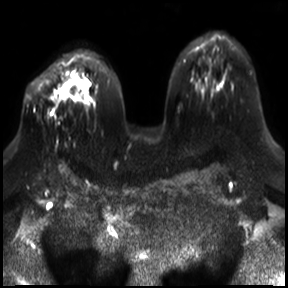
Breast MRI, one axial slice; position 20 of 30 along the scan axis; diffusion-weighted series; image 2 of 4 stored at this slice position (different b-values; order by instance number); 3 T; 4 mm slice thickness; 288 × 288 image matrix. Female patient.
Annotated regions visible in this slice (expert manual segmentation):
- tumour on diffusion-weighted imaging: bounding box <53,82,80,100> (left, top, right, bottom; pixels)